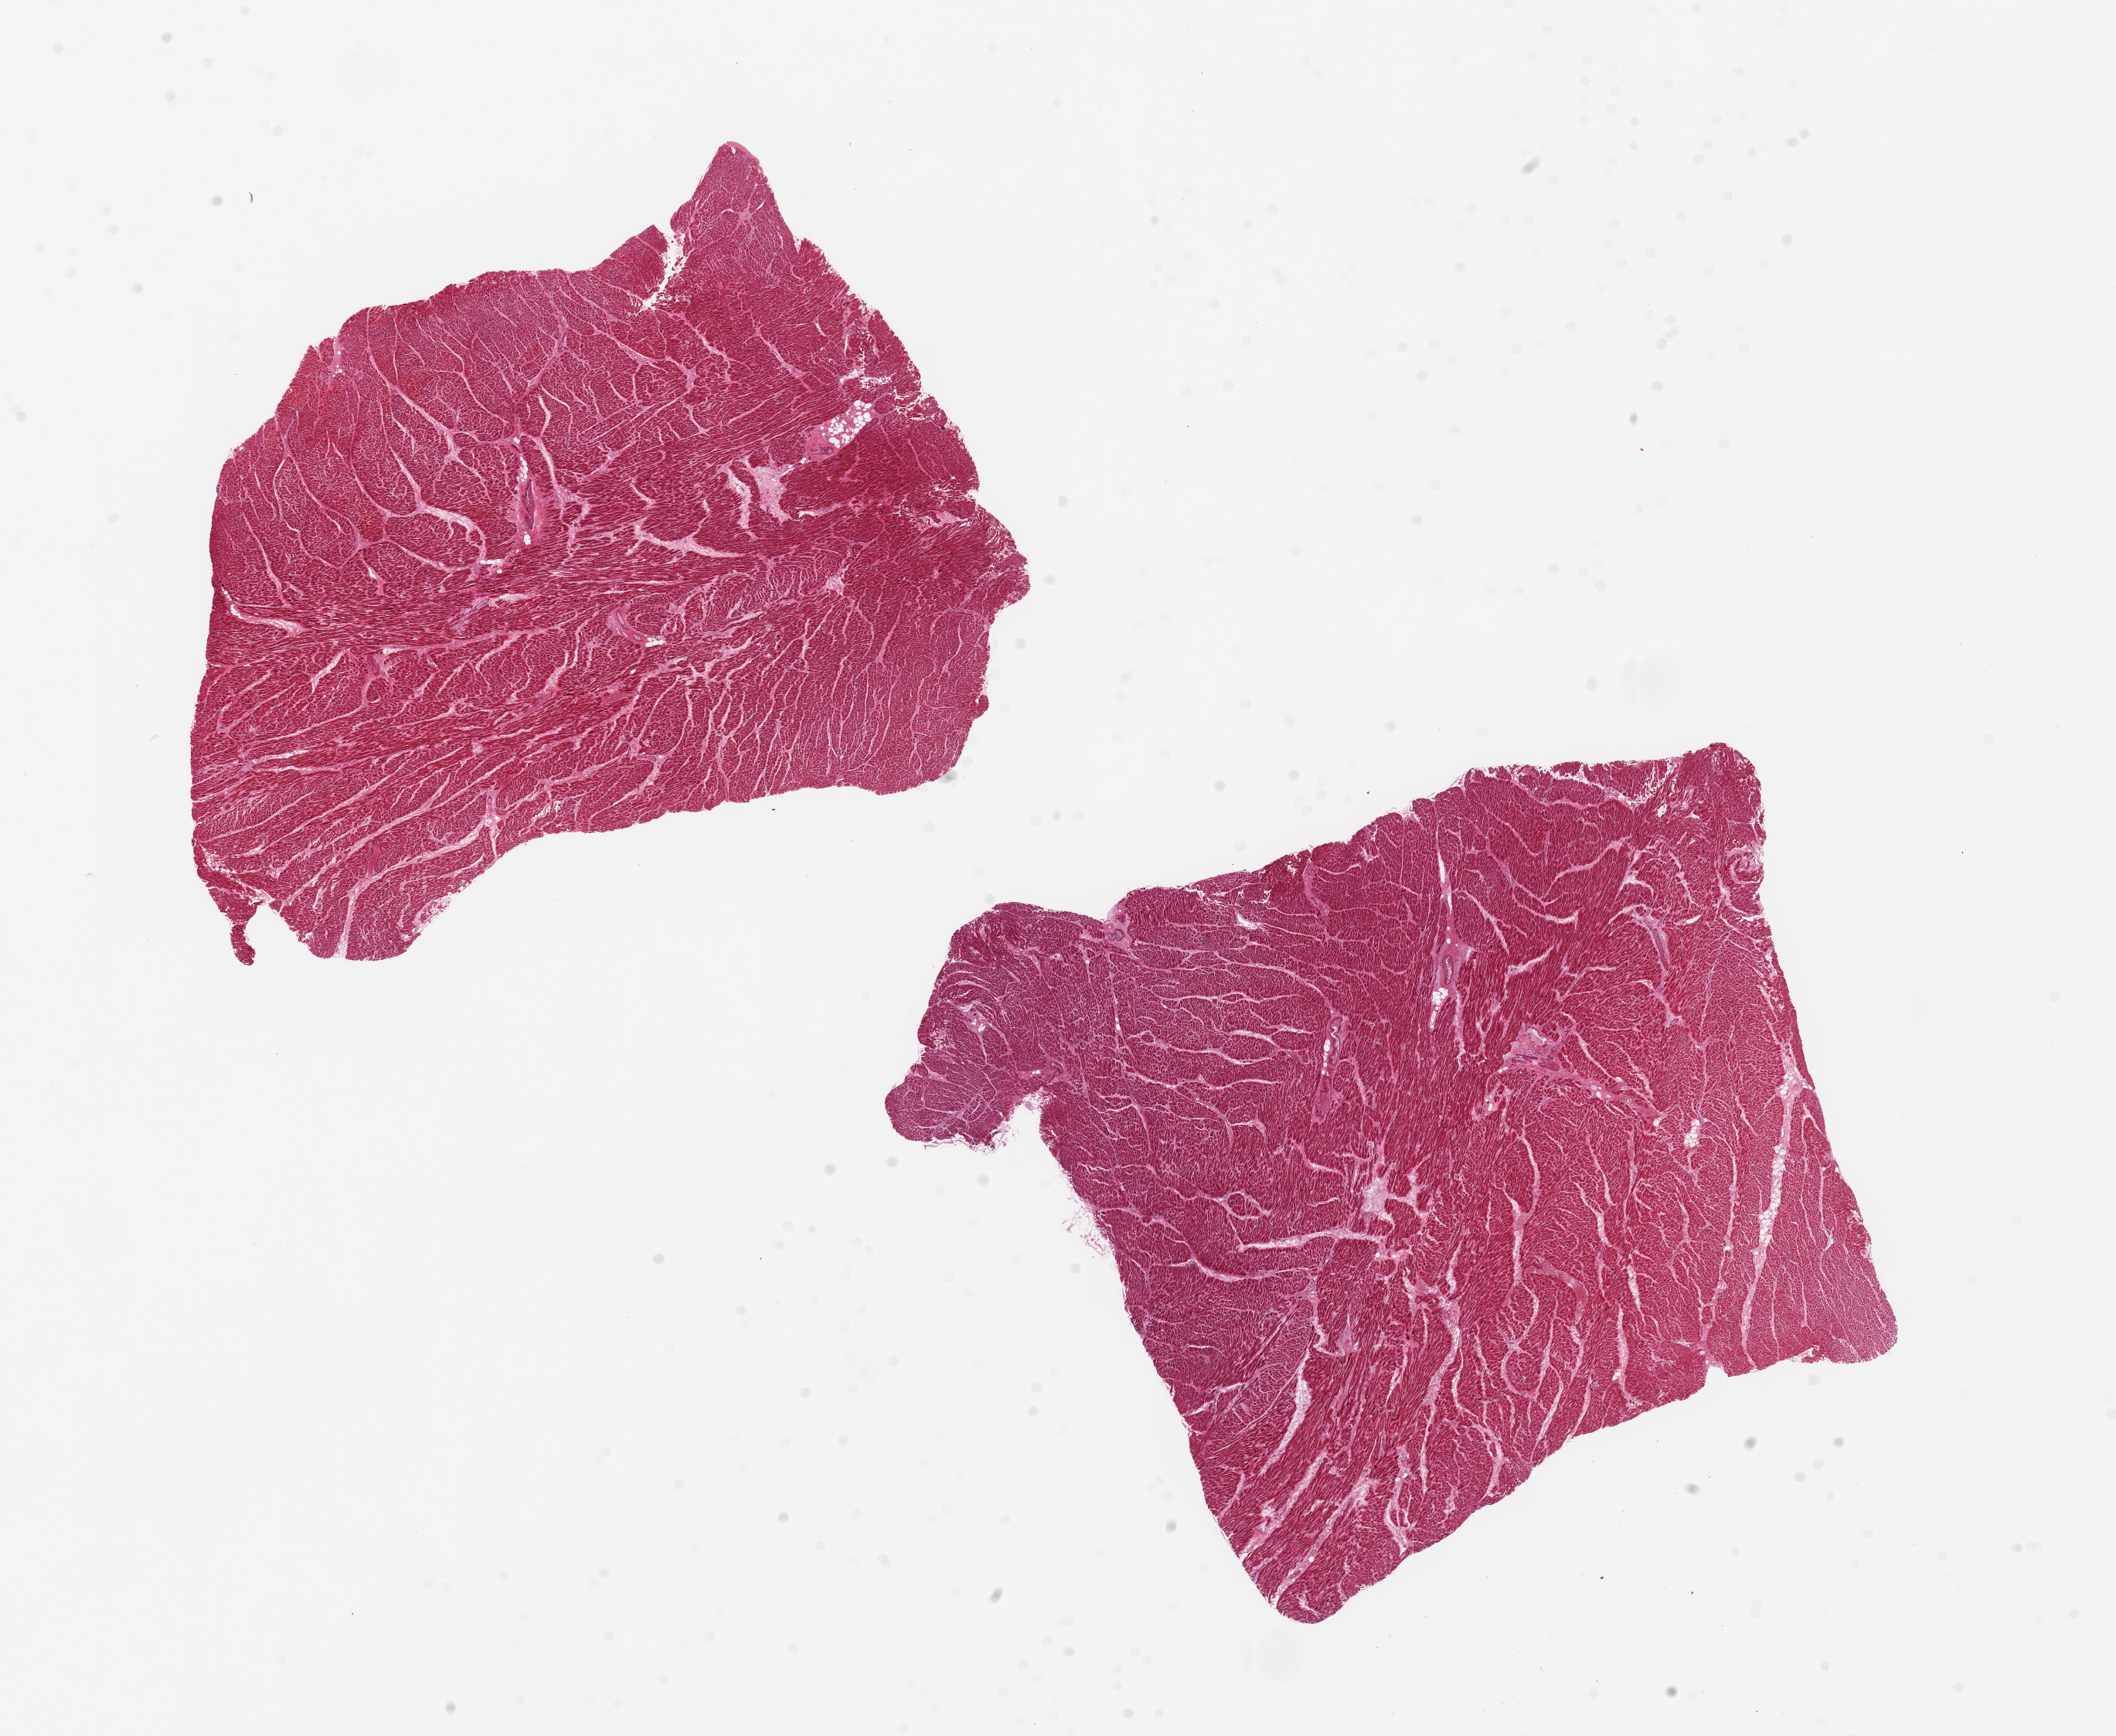
Whole-slide image, H&E stain — a low-resolution overview of the entire scanned area, about 21.7 x 17.8 mm (slide scanned at 20x). PAXgene-fixed paraffin-embedded (PFPE) section. Target tissue: heart. Tissue donor sample. Donor: female.
Review note (as recorded): 2 pieces, 9x7 & 9.5x8mm; Well dissected muscle.